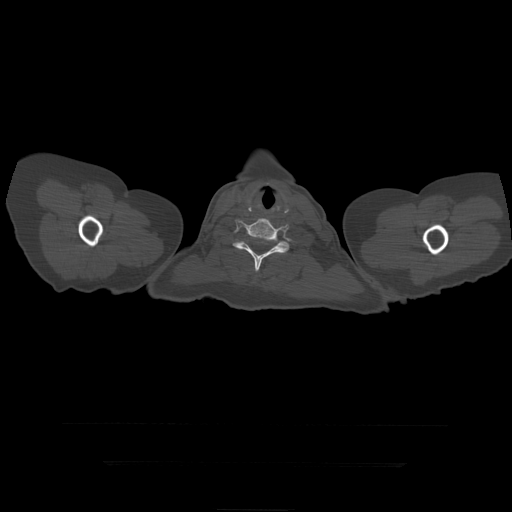
CT including the spine, one axial slice; slice 397 of 399 in the series (ordered by position); bone window (W 1800 / L 400 HU); 1.25 mm slice thickness; 512 × 512 image matrix, field of view 450 × 450 mm. Patient age 41 years. From the clinical record (not read from this slice): primary cancer: breast.
Annotated regions visible in this slice (semi-automatic segmentation, software-assisted and operator-edited):
- T1 vertebra: bounding box [x1, y1, x2, y2] px = [233, 240, 289, 250]